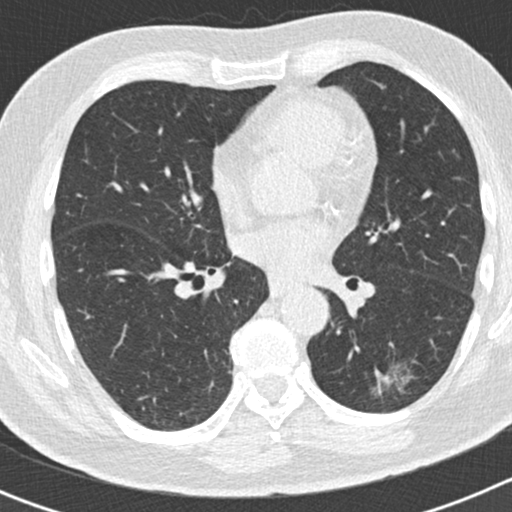
Axial slice from a low-dose chest CT screening exam, second screening round (one year after baseline), lung window (W 1500 / L -600 HU), 2 mm slice thickness, slice 87 of 186 in the series. Male, age 66 years at enrolment.
Lesion marked by an expert reader, bounding box (x1, y1, x2, y2) in pixels: (352, 340, 411, 408). Screening reader's record for this exam (one nodule recorded; not confirmed to be the boxed lesion): non-calcified nodule or mass ≥4 mm, left lower lobe, 50 × 33 mm, smooth margins, pre-existing on the prior screen: yes; interval growth: yes. Official screen result: positive, other. Participant outcome: lung cancer diagnosed 440 days after this screen — adenocarcinoma, NOS, left lower lobe, poorly differentiated (G3), stage IB (AJCC 6th edition), 38 mm at pathology.